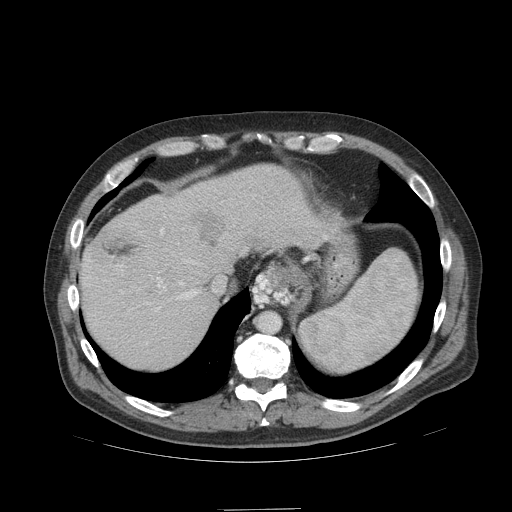
Contrast-enhanced abdominal CT (liver protocol), one axial slice. Slice 83 of 99 in the series (ordered by position). Reconstruction kernel STANDARD. Soft-tissue window (W 400 / L 40 HU). 2.5 mm slice thickness. 512 × 512 image matrix. Case-level facts recorded for this patient, not image findings: diagnosis: hepatocellular carcinoma (patient treated with transarterial chemoembolisation; whether this scan precedes or follows treatment is not stated here); TNM stage (as recorded): Stage-I; Child-Pugh class: A; tumour differentiation: no biopsy; tumour nodularity: uninodular.
Annotated regions visible in this slice (semi-automatic segmentation, software-assisted and operator-edited):
- liver parenchyma outside the tumour (the mass and vessels are separate outlines, so this box may not span the whole liver): bounding box [x1, y1, x2, y2] px = [80, 164, 336, 370]
- mass: [191, 209, 229, 247]
- liver vessels: [118, 228, 198, 311]